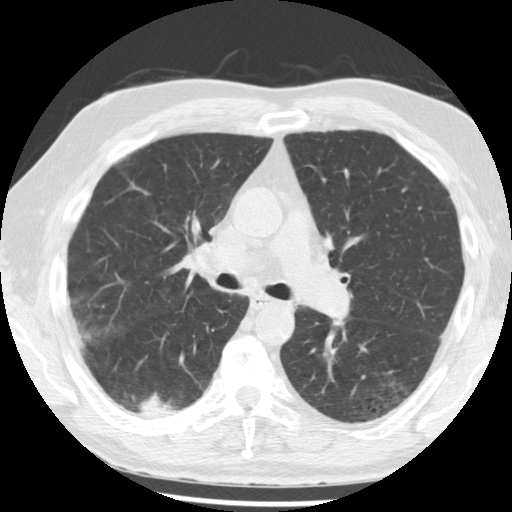
Low-dose screening chest CT, one axial slice. Position 125 of 221 along the scan axis. Lung window (W 1500 / L -600 HU). 512 × 512 image matrix, field of view 350 × 350 mm.
Structures marked on this image (manually delineated by an expert):
- lesion 1 (tumor, lower lobe of right lung): bounding box <140,394,181,417> (left, top, right, bottom; pixels)